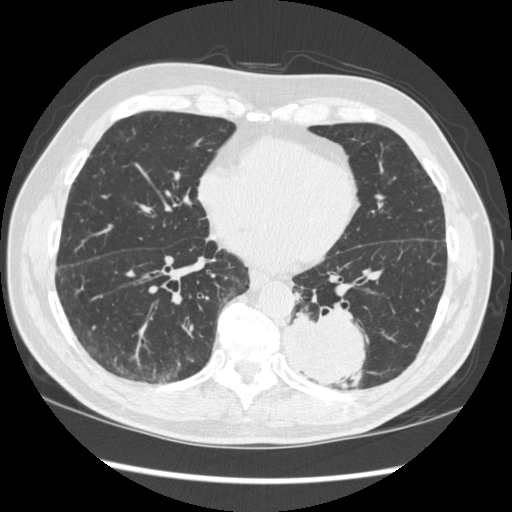
Low-dose screening chest CT, axial slice. First (baseline) screen. Lung window (W 1500 / L -600 HU). 1.25 mm slice thickness. Standard (soft-tissue) reconstruction kernel (STANDARD). Slice 127 of 348 in the series. Male, age 72 years at enrolment.
Lesion marked by an expert reader, bounding box <272,298,376,387> (left, top, right, bottom; pixels). The screening reader recorded 2 non-calcified nodules or masses ≥4 mm on this exam (left lower lobe, right middle lobe); which of them this box marks is not recorded. Official screen result: positive, change unspecified: nodule(s) >= 4 mm or enlarging nodule(s), mass(es), or other non-specific abnormalities suspicious for lung cancer. Participant outcome: lung cancer diagnosed 37 days after this screen — squamous cell carcinoma, NOS, left lower lobe, stage IIIA (AJCC 6th edition), 60 mm at pathology.